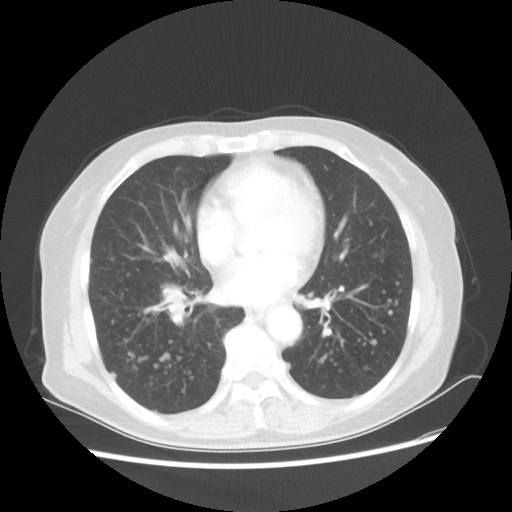
Chest CT, one axial slice. Position 24 of 56 along the scan axis. Reconstruction kernel STANDARD. 80 kVp. Lung window (W 1500 / L -600 HU). 512 × 512 image matrix, field of view 360 × 360 mm. Female patient, age 68 years. From the clinical record (not read from this slice): clinical TNM (as recorded): T1c N3 M0.
Structures marked on this image (rectangle marked by the reading radiologist):
- lung tumour (recorded histology: squamous cell carcinoma): bounding box (x1, y1, x2, y2) in pixels: (151, 276, 191, 300)